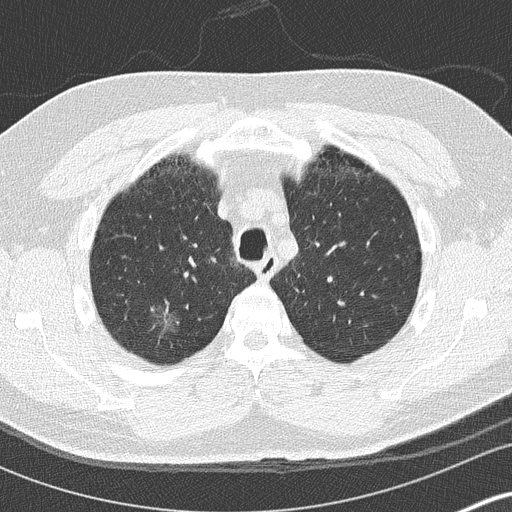
Axial slice from a low-dose chest CT screening exam; first (baseline) screen; lung window (W 1500 / L -600 HU); 2 mm slice thickness; slice 33 of 136 in the series; 512 × 512 image matrix. Male, age 59 years at enrolment. Current smoker at enrolment.
- Lesion marked by an expert reader, bounding box [x1, y1, x2, y2] px = [143, 292, 195, 343].
- The exam's reader record, not a measurement of the box and not confirmed to be the same lesion: non-calcified nodule or mass ≥4 mm, right upper lobe, 16 × 16 mm, ground glass attenuation.
- Official screen result: positive, change unspecified: nodule(s) >= 4 mm or enlarging nodule(s), mass(es), or other non-specific abnormalities suspicious for lung cancer.